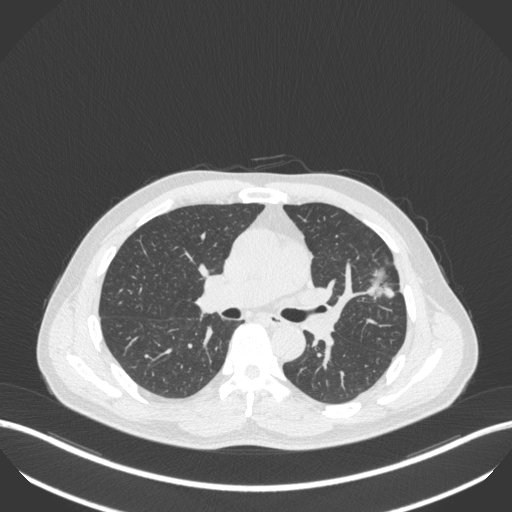
Chest CT, one axial slice; slice 231 of 418 in the series (ordered by position); 120 kVp; lung window (W 1500 / L -600 HU); 1 mm slice thickness; 512 × 512 image matrix, field of view 400 × 400 mm. Patient: male, 55 years. From the clinical record (not read from this slice): clinical TNM (as recorded): T1c N0 M0; histopathological grade: G2-3.
Annotated regions visible in this slice (bounding box drawn by a radiologist):
- lung tumour (recorded histology: adenocarcinoma): bounding box (x1, y1, x2, y2) in pixels: (365, 264, 402, 301)